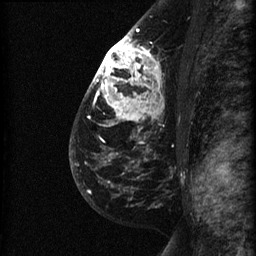
Breast MRI (dynamic contrast-enhanced), one sagittal slice. Slice 42 of 60 in the series (ordered by position). Dynamic contrast-enhanced series, image 2 of 3 at this slice position (ordered by acquisition). 1.5 T. TE 4.2 ms, TR 22.7 ms. 256 × 256 image matrix, field of view 180 × 180 mm. Female patient, age 48 years. From the clinical record (not read from this slice): setting: breast cancer imaged before/during neoadjuvant chemotherapy; receptor status: triple-negative.
Annotated regions visible in this slice (semi-automatically segmented with operator editing):
- analysis volume of interest (the breast-tissue region the enhancement analysis was run in; not a lesion): bounding box <89,27,183,180> (left, top, right, bottom; pixels)
- tumour enhancement mask (voxels above the 90 % enhancement threshold inside the analysis volume of interest): <93,29,157,160>